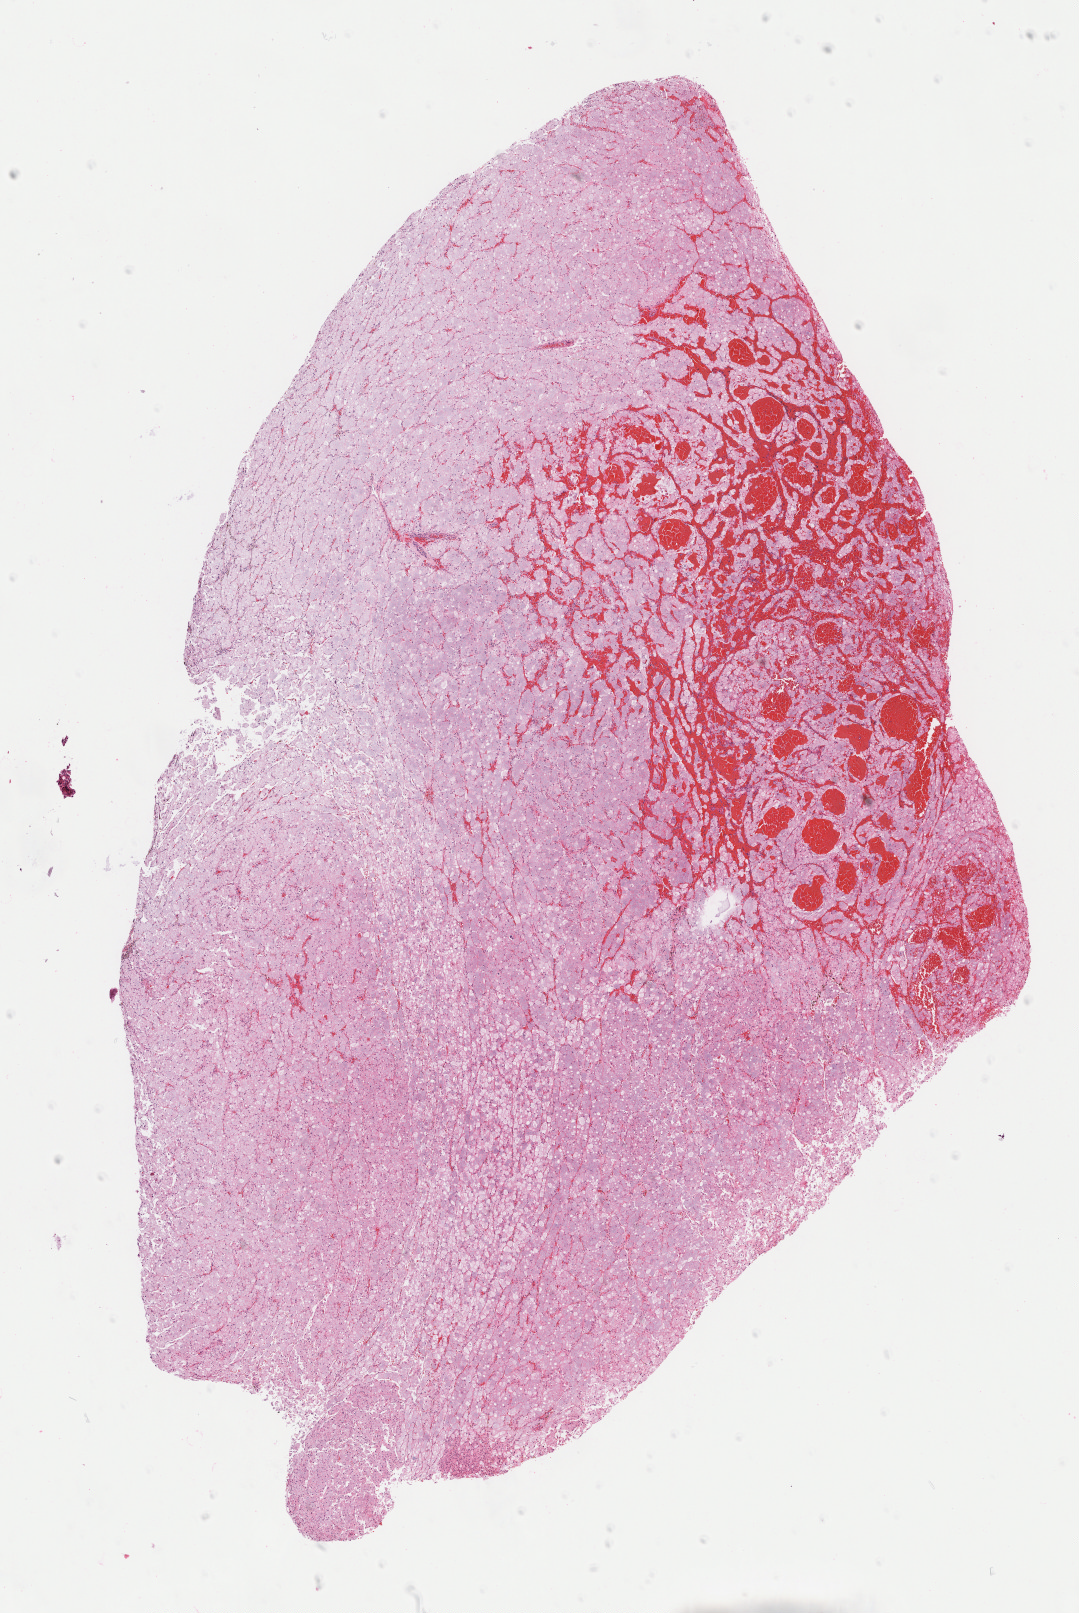
Digitized H&E tissue section (whole slide) — shown as a low-resolution overview of the whole scanned area (about 8.7 x 13.0 mm, slide scanned at 40x). Formalin-fixed paraffin-embedded (FFPE) diagnostic section. Kidney, primary tumour sample. Female, age 46 years at initial diagnosis.
AJCC pathologic stage: III (6th edition). TNM: T3a NX. Pathologic diagnosis: Renal cell carcinoma, chromophobe type.